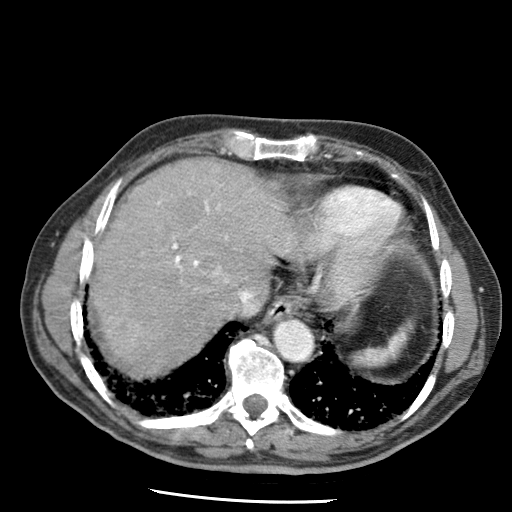
Contrast-enhanced abdominal CT (liver protocol), one axial slice. Position 56 of 79 along the scan axis. Reconstruction kernel STANDARD. 120 kVp. Soft-tissue window (W 400 / L 40 HU). 512 × 512 image matrix, field of view 320 × 320 mm. From the clinical record (not read from this slice): diagnosis: hepatocellular carcinoma (patient treated with transarterial chemoembolisation; whether this scan precedes or follows treatment is not stated here); TNM stage (as recorded): Stage-IIIA; Child-Pugh class: A; tumour nodularity: multinodular; tumour size: 7 cm.
Structures marked on this image (semi-automatically segmented with operator editing):
- abdominal aorta: bounding box [x1, y1, x2, y2] px = [275, 322, 312, 360]
- liver parenchyma outside the tumour (the mass and vessels are separate outlines, so this box may not span the whole liver): [90, 158, 296, 374]
- liver vessels: [157, 184, 289, 283]